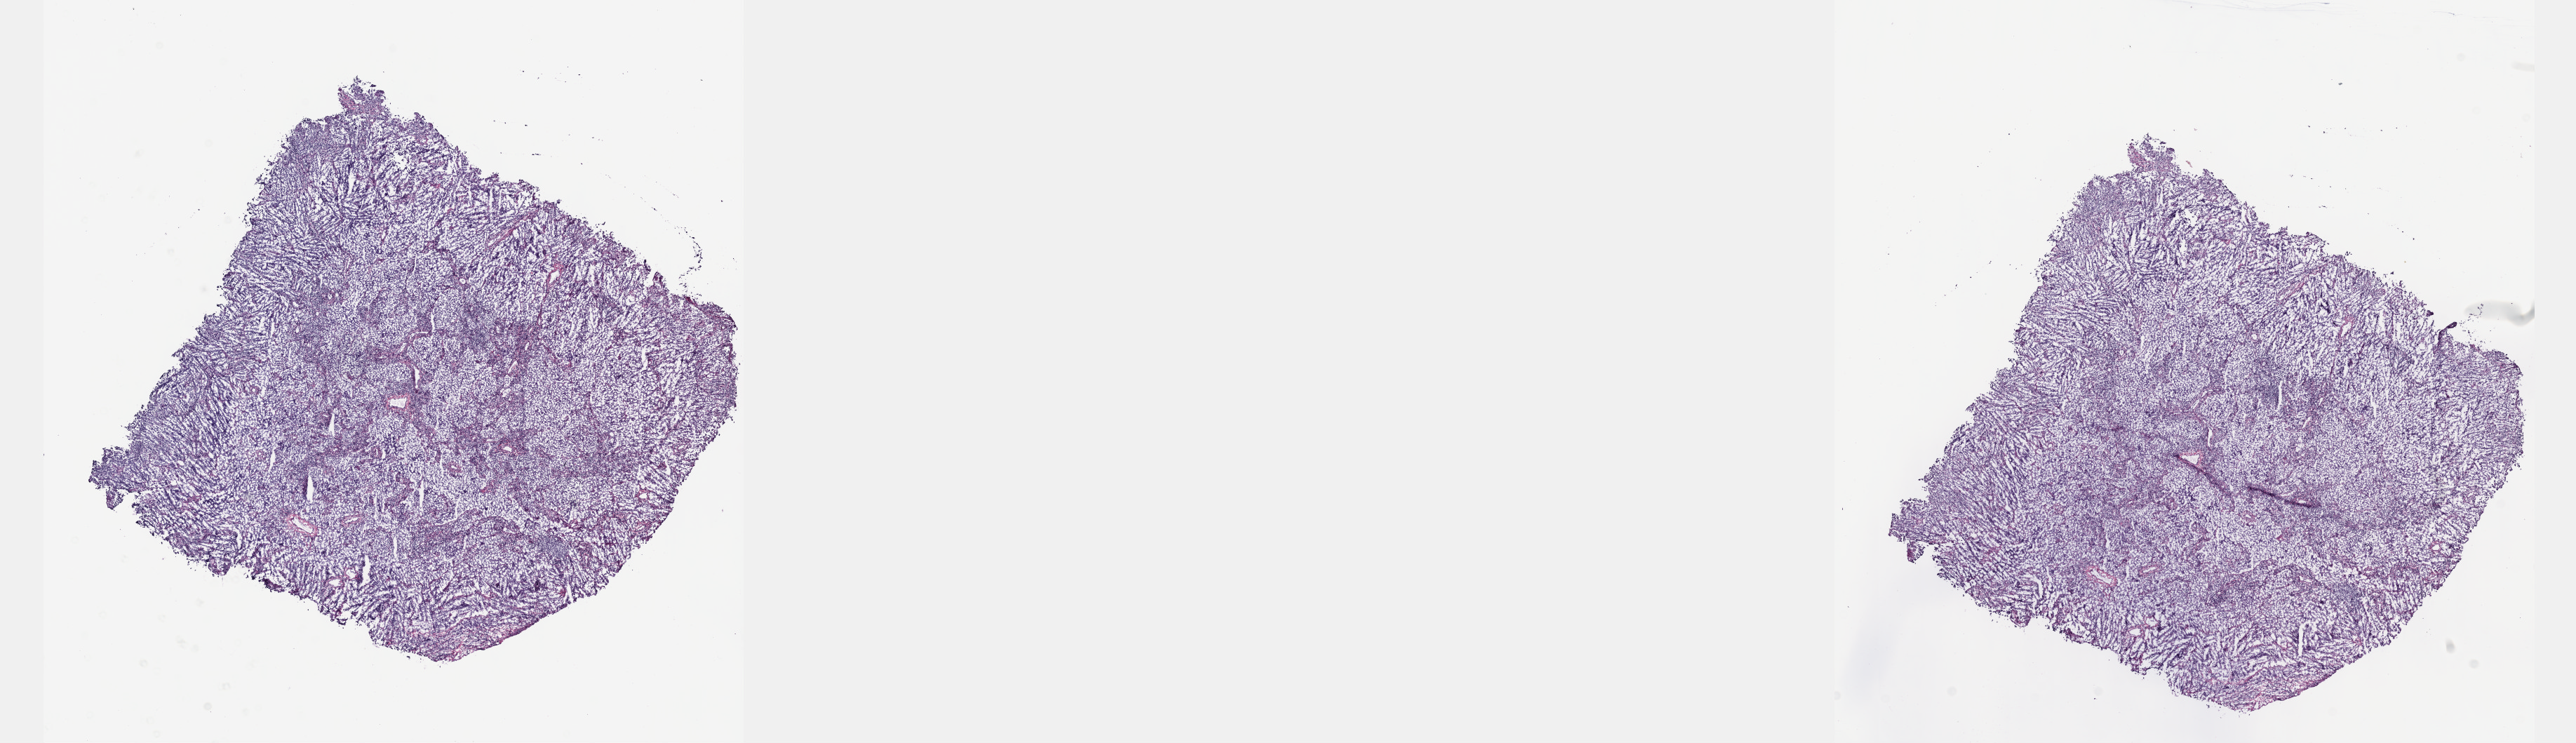
H&E whole-slide image, whole scanned area (about 29.7 x 8.6 mm, acquisition: 40x scan) shown as a low-resolution overview; frozen section from the top of the tissue portion; testis, additional new primary tumour sample. Male patient; age at initial diagnosis 31 years. Pathologist review of this section (percent, as recorded): tumour cells 100%, tumour nuclei 75%, normal cells 0%, stromal cells 0%, necrosis 0%. Inflammatory infiltration, as recorded: lymphocyte infiltration 1%, monocyte infiltration 0%, neutrophil infiltration 0%.
This section: additional new primary tumour. Patient diagnosis: Seminoma, NOS.